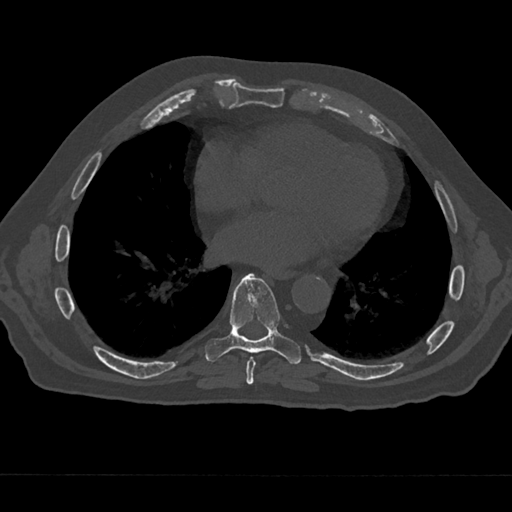
CT including the spine, one axial slice; position 324 of 797 along the scan axis; reconstruction kernel Br40s/3; bone window (W 1800 / L 400 HU); 0.5 mm slice thickness; 512 × 512 image matrix. Patient: male, 75 years. Case-level facts recorded for this patient, not image findings: primary cancer: renal.
Annotated regions visible in this slice (semi-automatically segmented with operator editing):
- T7 vertebra: bounding box [x1, y1, x2, y2] px = [244, 356, 258, 385]
- T8 vertebra: [205, 273, 301, 365]